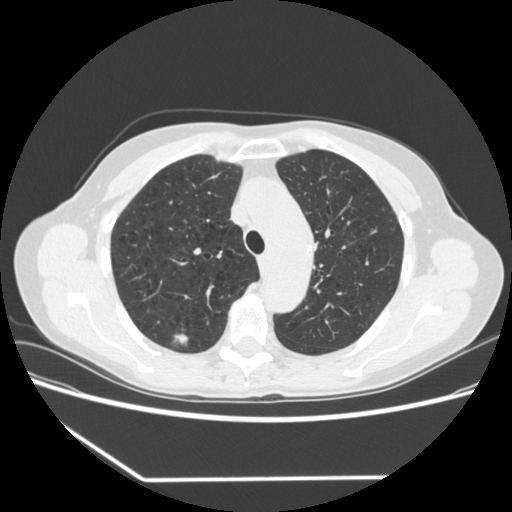
Axial slice from a low-dose chest CT screening exam, baseline annual screen, lung window (W 1500 / L -600 HU), standard (soft-tissue) reconstruction kernel (STANDARD), slice 248 of 323 in the series, 512 × 512 image matrix. Female participant, aged 67 years at enrolment. Current smoker at enrolment.
Lesion marked by an expert reader, bounding box [x1, y1, x2, y2] px = [153, 322, 198, 356]. The screening reader recorded 2 non-calcified nodules or masses ≥4 mm on this exam; which of them this box marks is not recorded. Official screen result: positive, change unspecified: nodule(s) >= 4 mm or enlarging nodule(s), mass(es), or other non-specific abnormalities suspicious for lung cancer. Later outcome: lung cancer diagnosed 29 days after this screen — adenocarcinoma, NOS, right upper lobe, moderately differentiated (G2), stage IA (AJCC 6th edition), 24 mm at pathology.